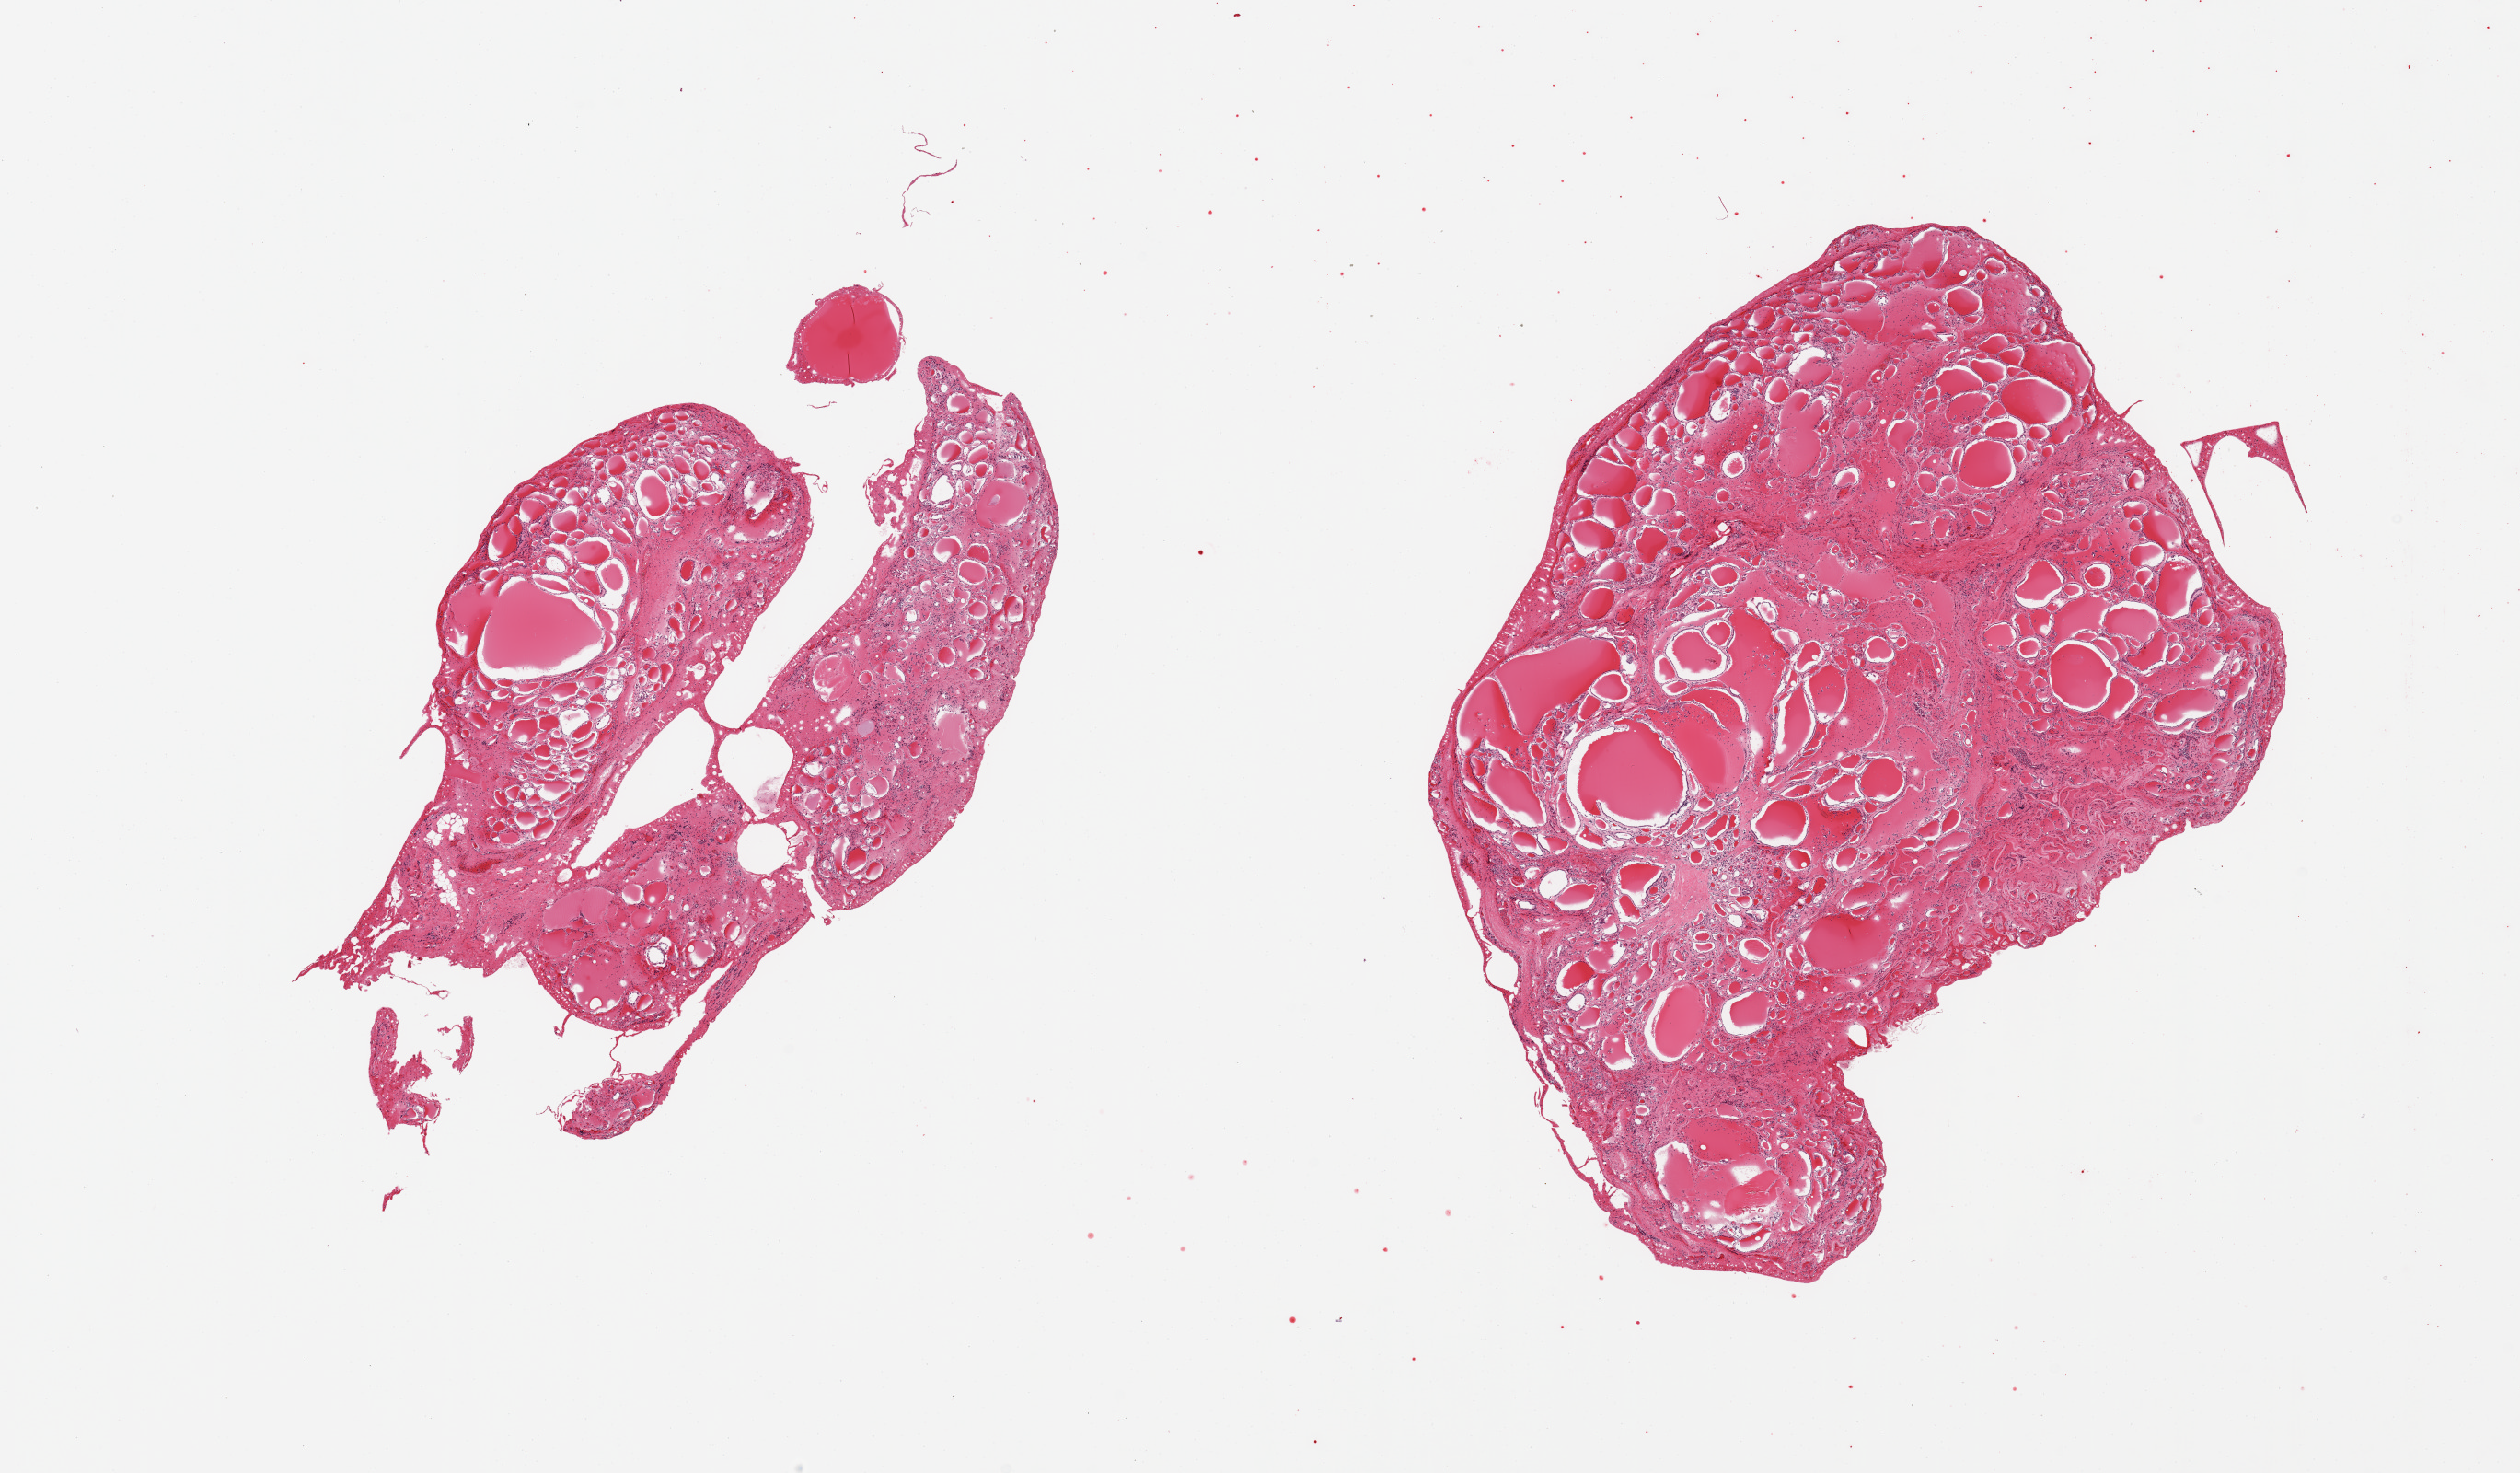
Hematoxylin and eosin (H&E) whole-slide image — shown as a low-resolution overview of the whole scanned area (about 21.7 x 12.7 mm), PAXgene-fixed paraffin-embedded (PFPE) section, section of thyroid (target tissue), donor tissue sample.
• pathologist's review note for this sample: 2 pieces; interstitial fibrosis with nodules composed of variably sized follicles